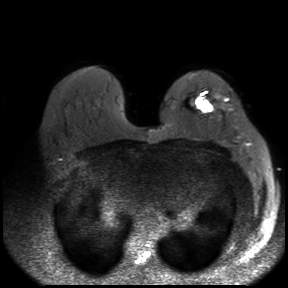
Breast MRI, one axial slice. Slice 20 of 30 in the series (ordered by position). Diffusion-weighted series; image 2 of 4 stored at this slice position (different b-values; order by instance number). 3 T. 288 × 288 image matrix, field of view 360 × 360 mm. Female patient.
Annotated regions visible in this slice (outlined manually by an expert reader):
- tumour on diffusion-weighted imaging: bounding box <195,97,212,112> (left, top, right, bottom; pixels)